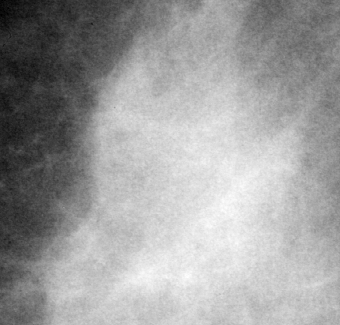
Crop from a digitized film mammogram around one marked abnormality; right breast; MLO view.
Marked abnormality: mass, shape irregular / architectural distortion, margins obscured / ill defined; BI-RADS assessment category 4; pathology (as recorded): malignant.